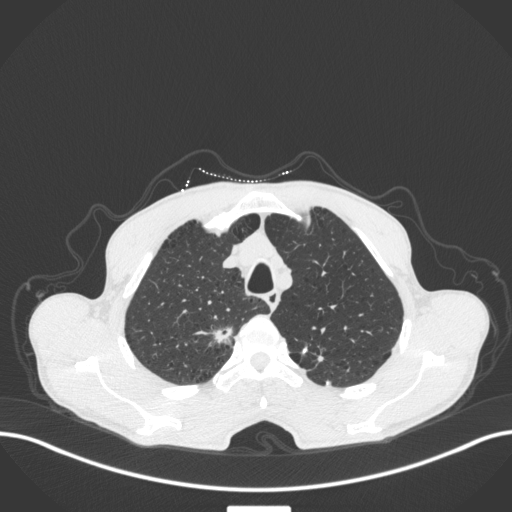
Chest CT, one axial slice. Position 352 of 445 along the scan axis. Reconstruction kernel B31f. Lung window (W 1500 / L -600 HU). 1 mm slice thickness. 512 × 512 image matrix, field of view 400 × 400 mm. Male patient, age 70 years. From the clinical record (not read from this slice): clinical TNM (as recorded): T1a N0 M0.
Annotated regions visible in this slice (bounding box drawn by a radiologist):
- lung tumour (recorded histology: adenocarcinoma): bounding box (x1, y1, x2, y2) in pixels: (192, 321, 237, 350)